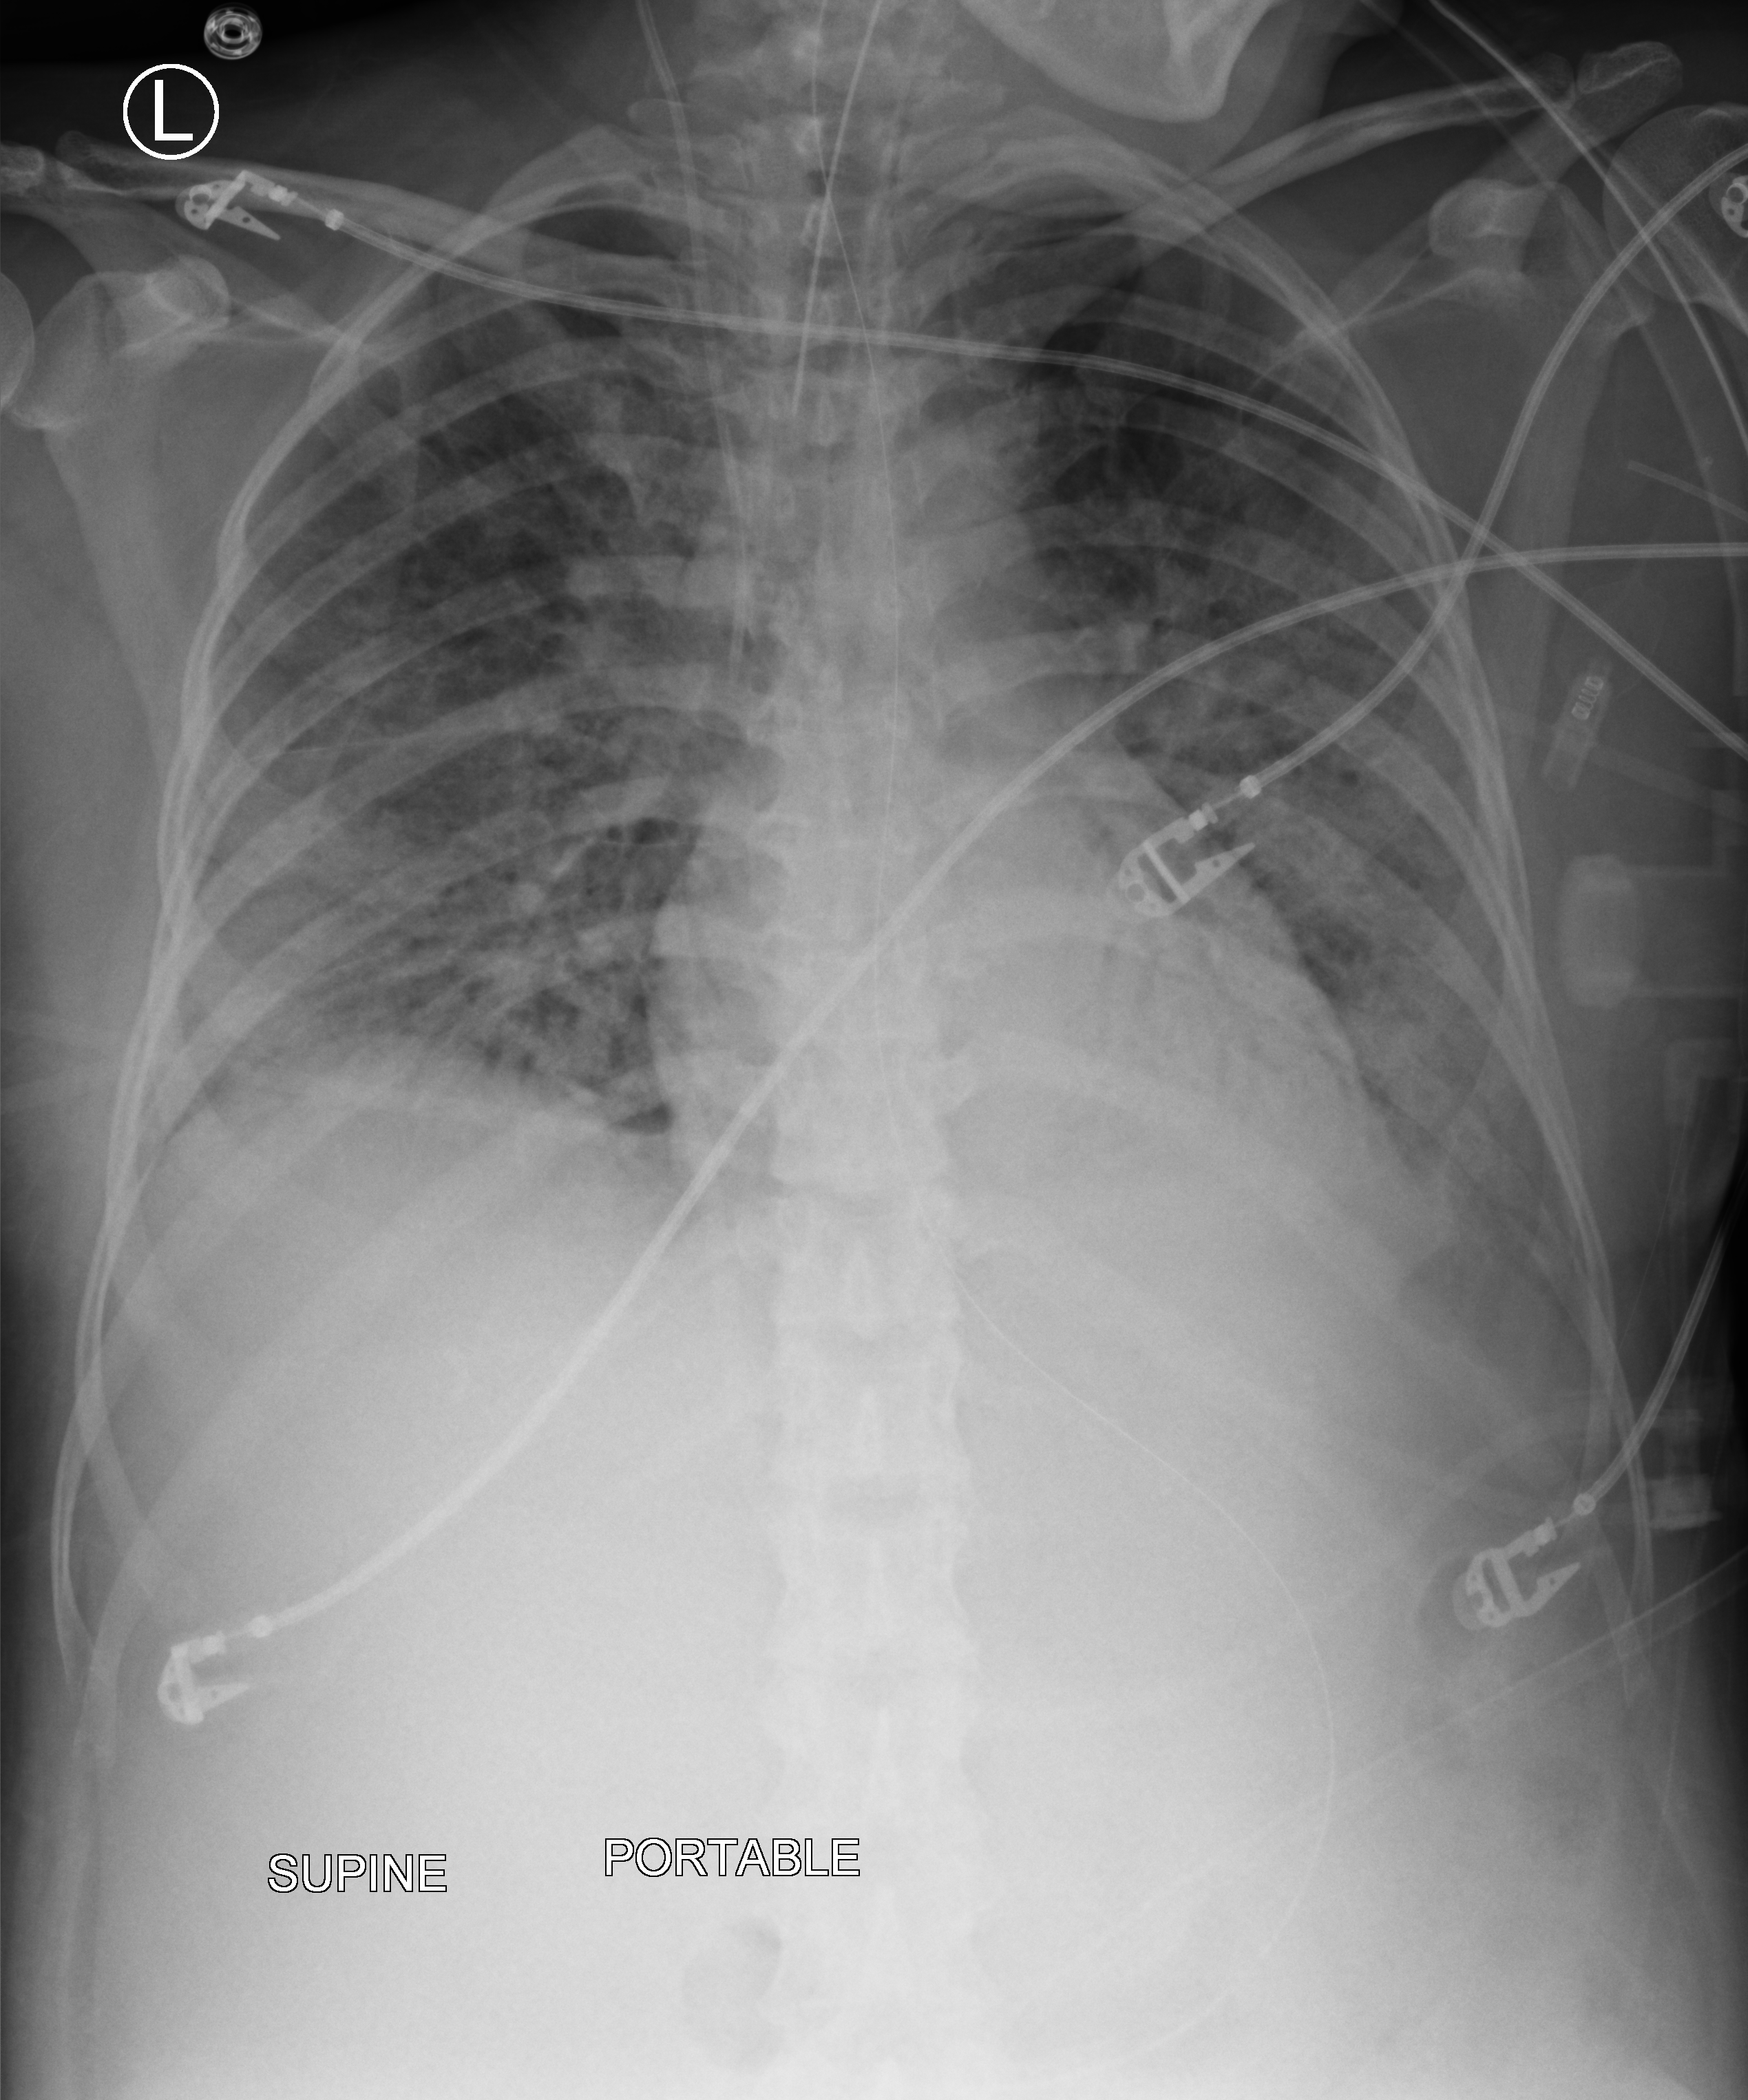
Chest X-ray (portable). Patient hospitalised with COVID-19; female, aged 18–59 years.
Hospital-stay facts (about this admission, not read from this image; timing relative to this image not recorded):
- admitted to intensive care during this hospital stay: yes
- diabetes (admission record): no